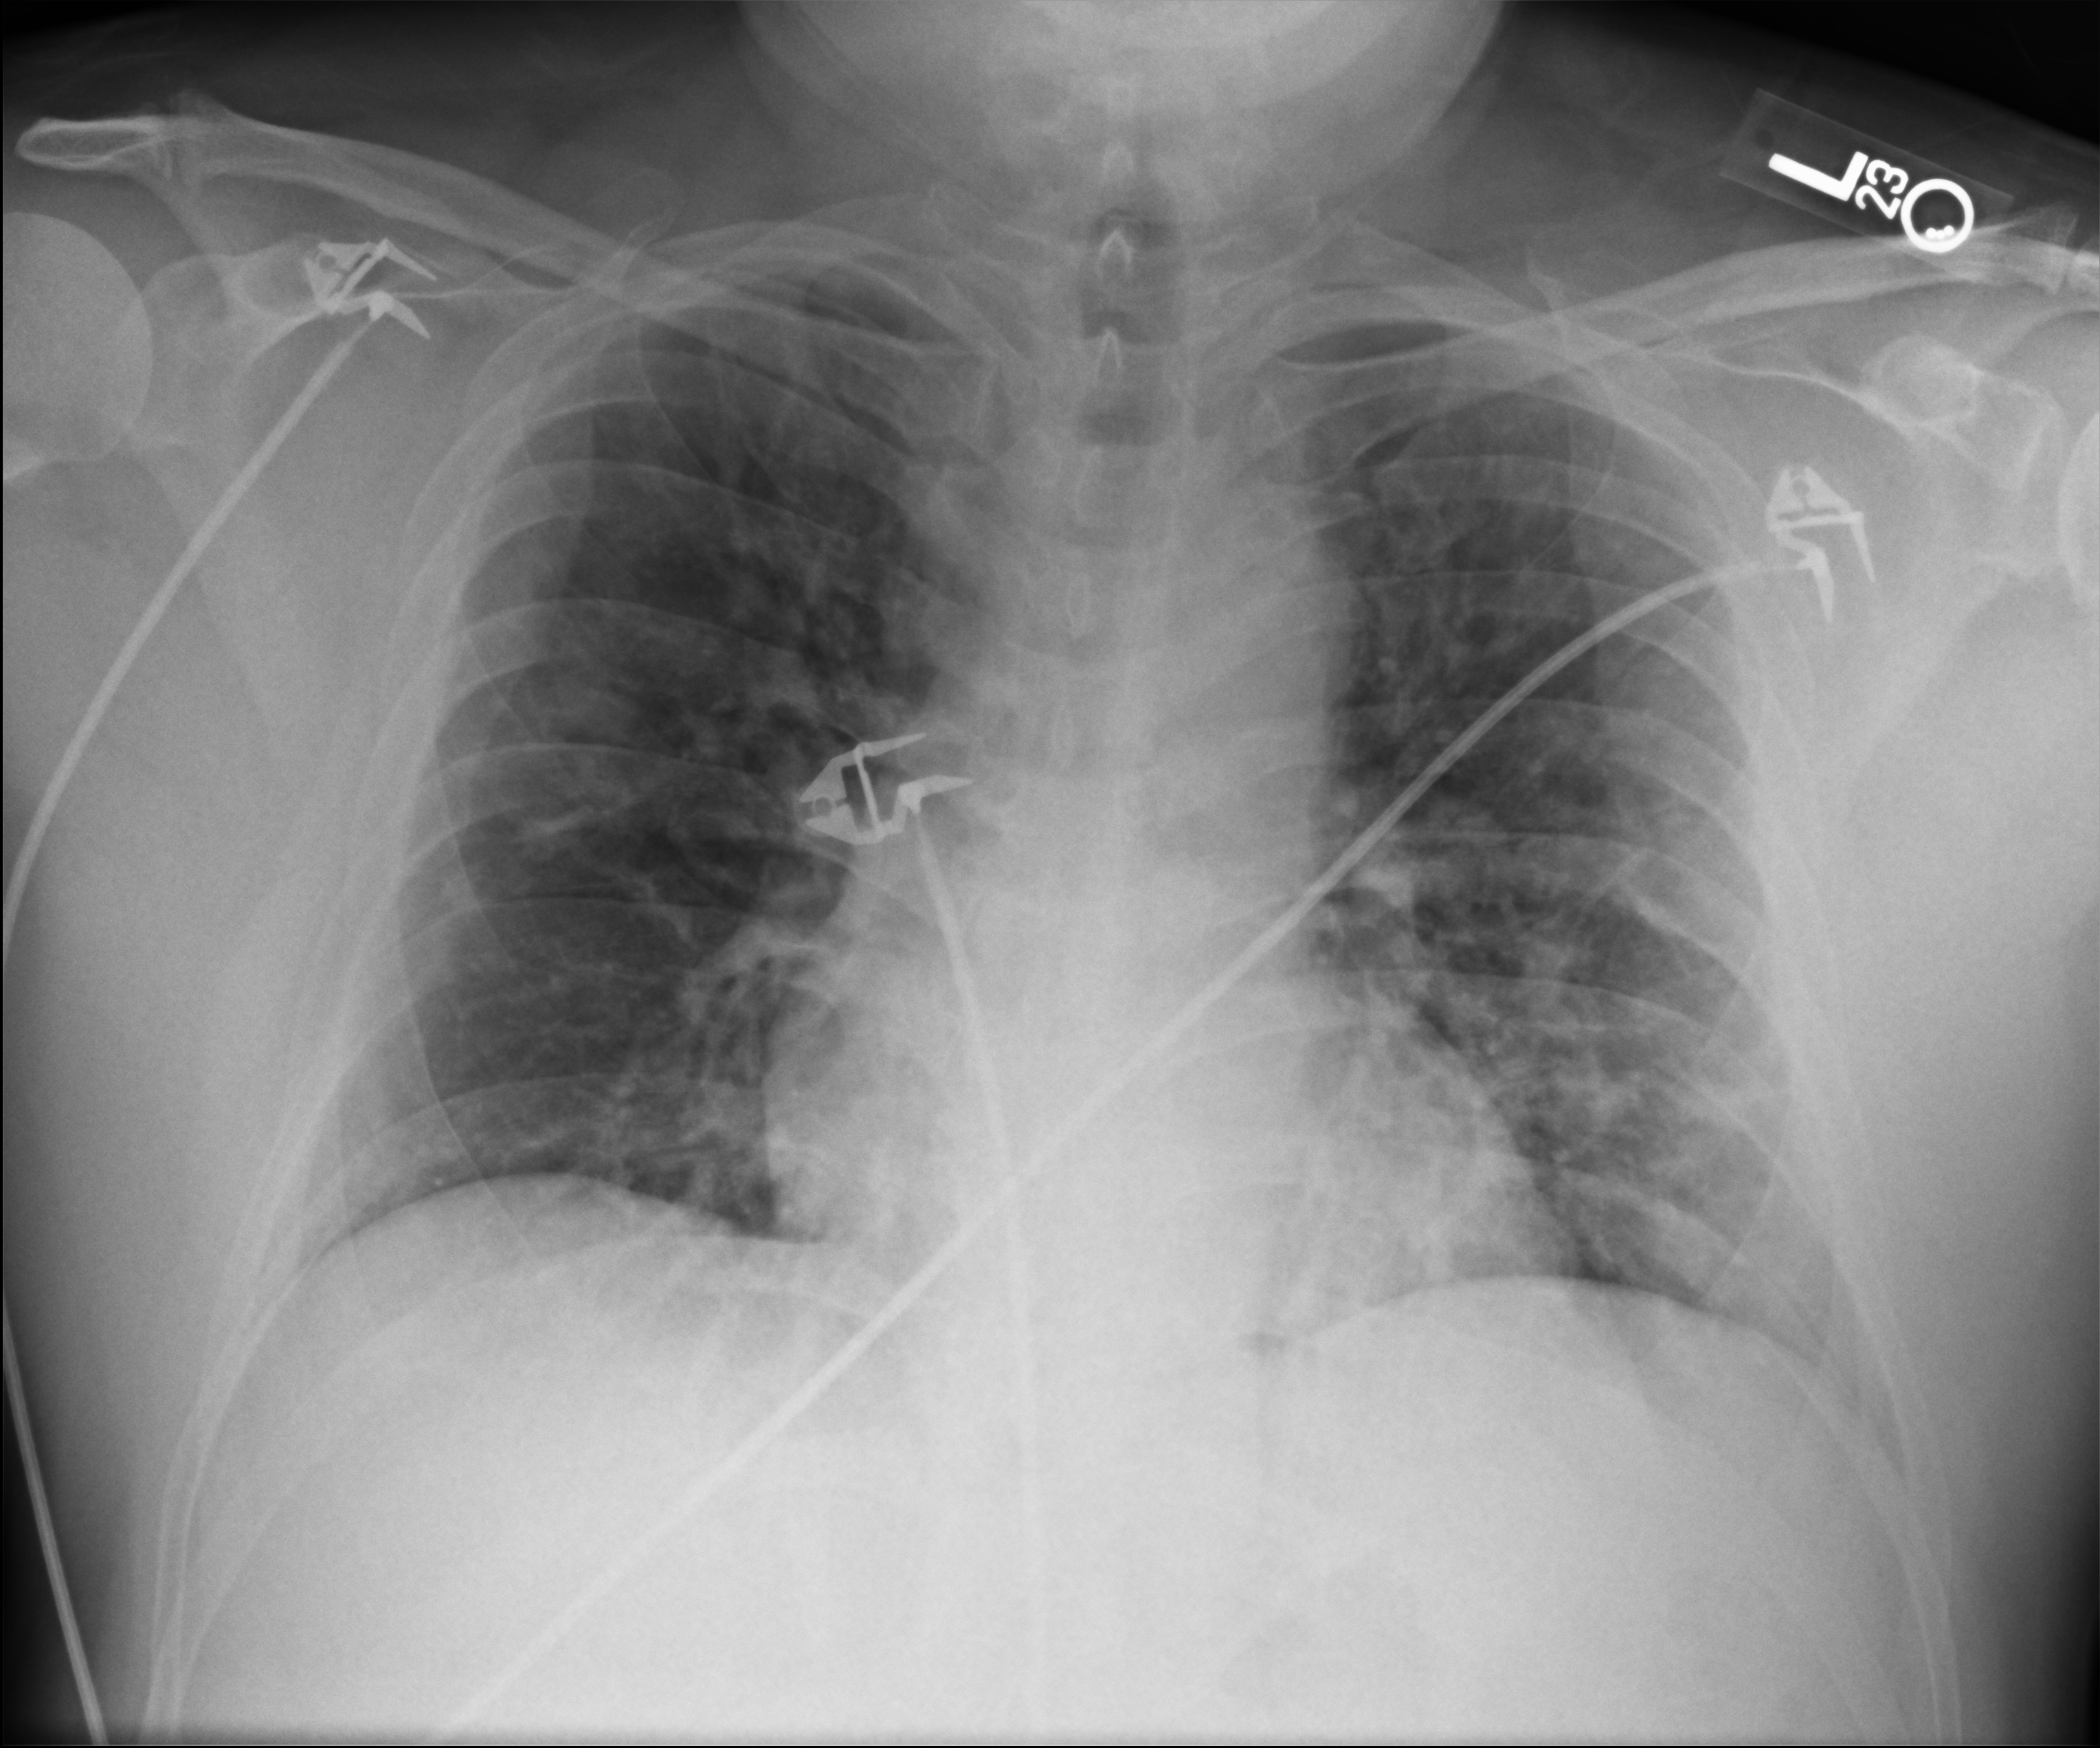
Chest X-ray (portable); anteroposterior (AP) projection. Patient hospitalised with COVID-19; male, aged 18–59 years.
From the hospital-stay record, not from the radiograph (when in the stay this image was taken is not recorded): hypertension (admission record): no; mechanically ventilated during this hospital stay: no.